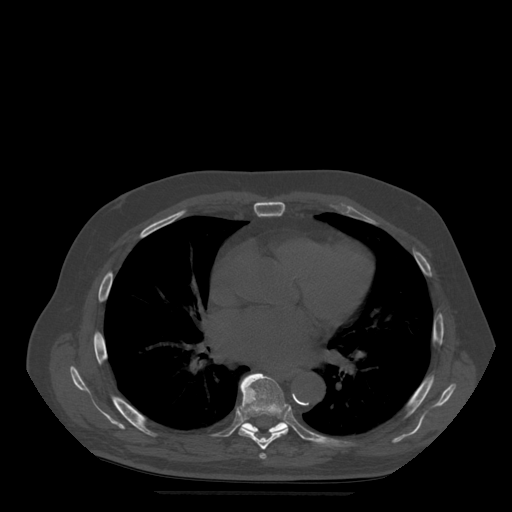
CT including the spine, one axial slice. Slice 326 of 522 in the series (ordered by position). Bone window (W 1800 / L 400 HU). 1.25 mm slice thickness. 512 × 512 image matrix, field of view 420 × 420 mm. Patient age 72 years. From the clinical record (not read from this slice): primary cancer: prostate.
Annotated regions visible in this slice (semi-automatic segmentation, software-assisted and operator-edited):
- T6 vertebra: bounding box (x1, y1, x2, y2) in pixels: (260, 454, 267, 459)
- T7 vertebra: (239, 374, 289, 450)
- T8 vertebra: (241, 375, 288, 433)